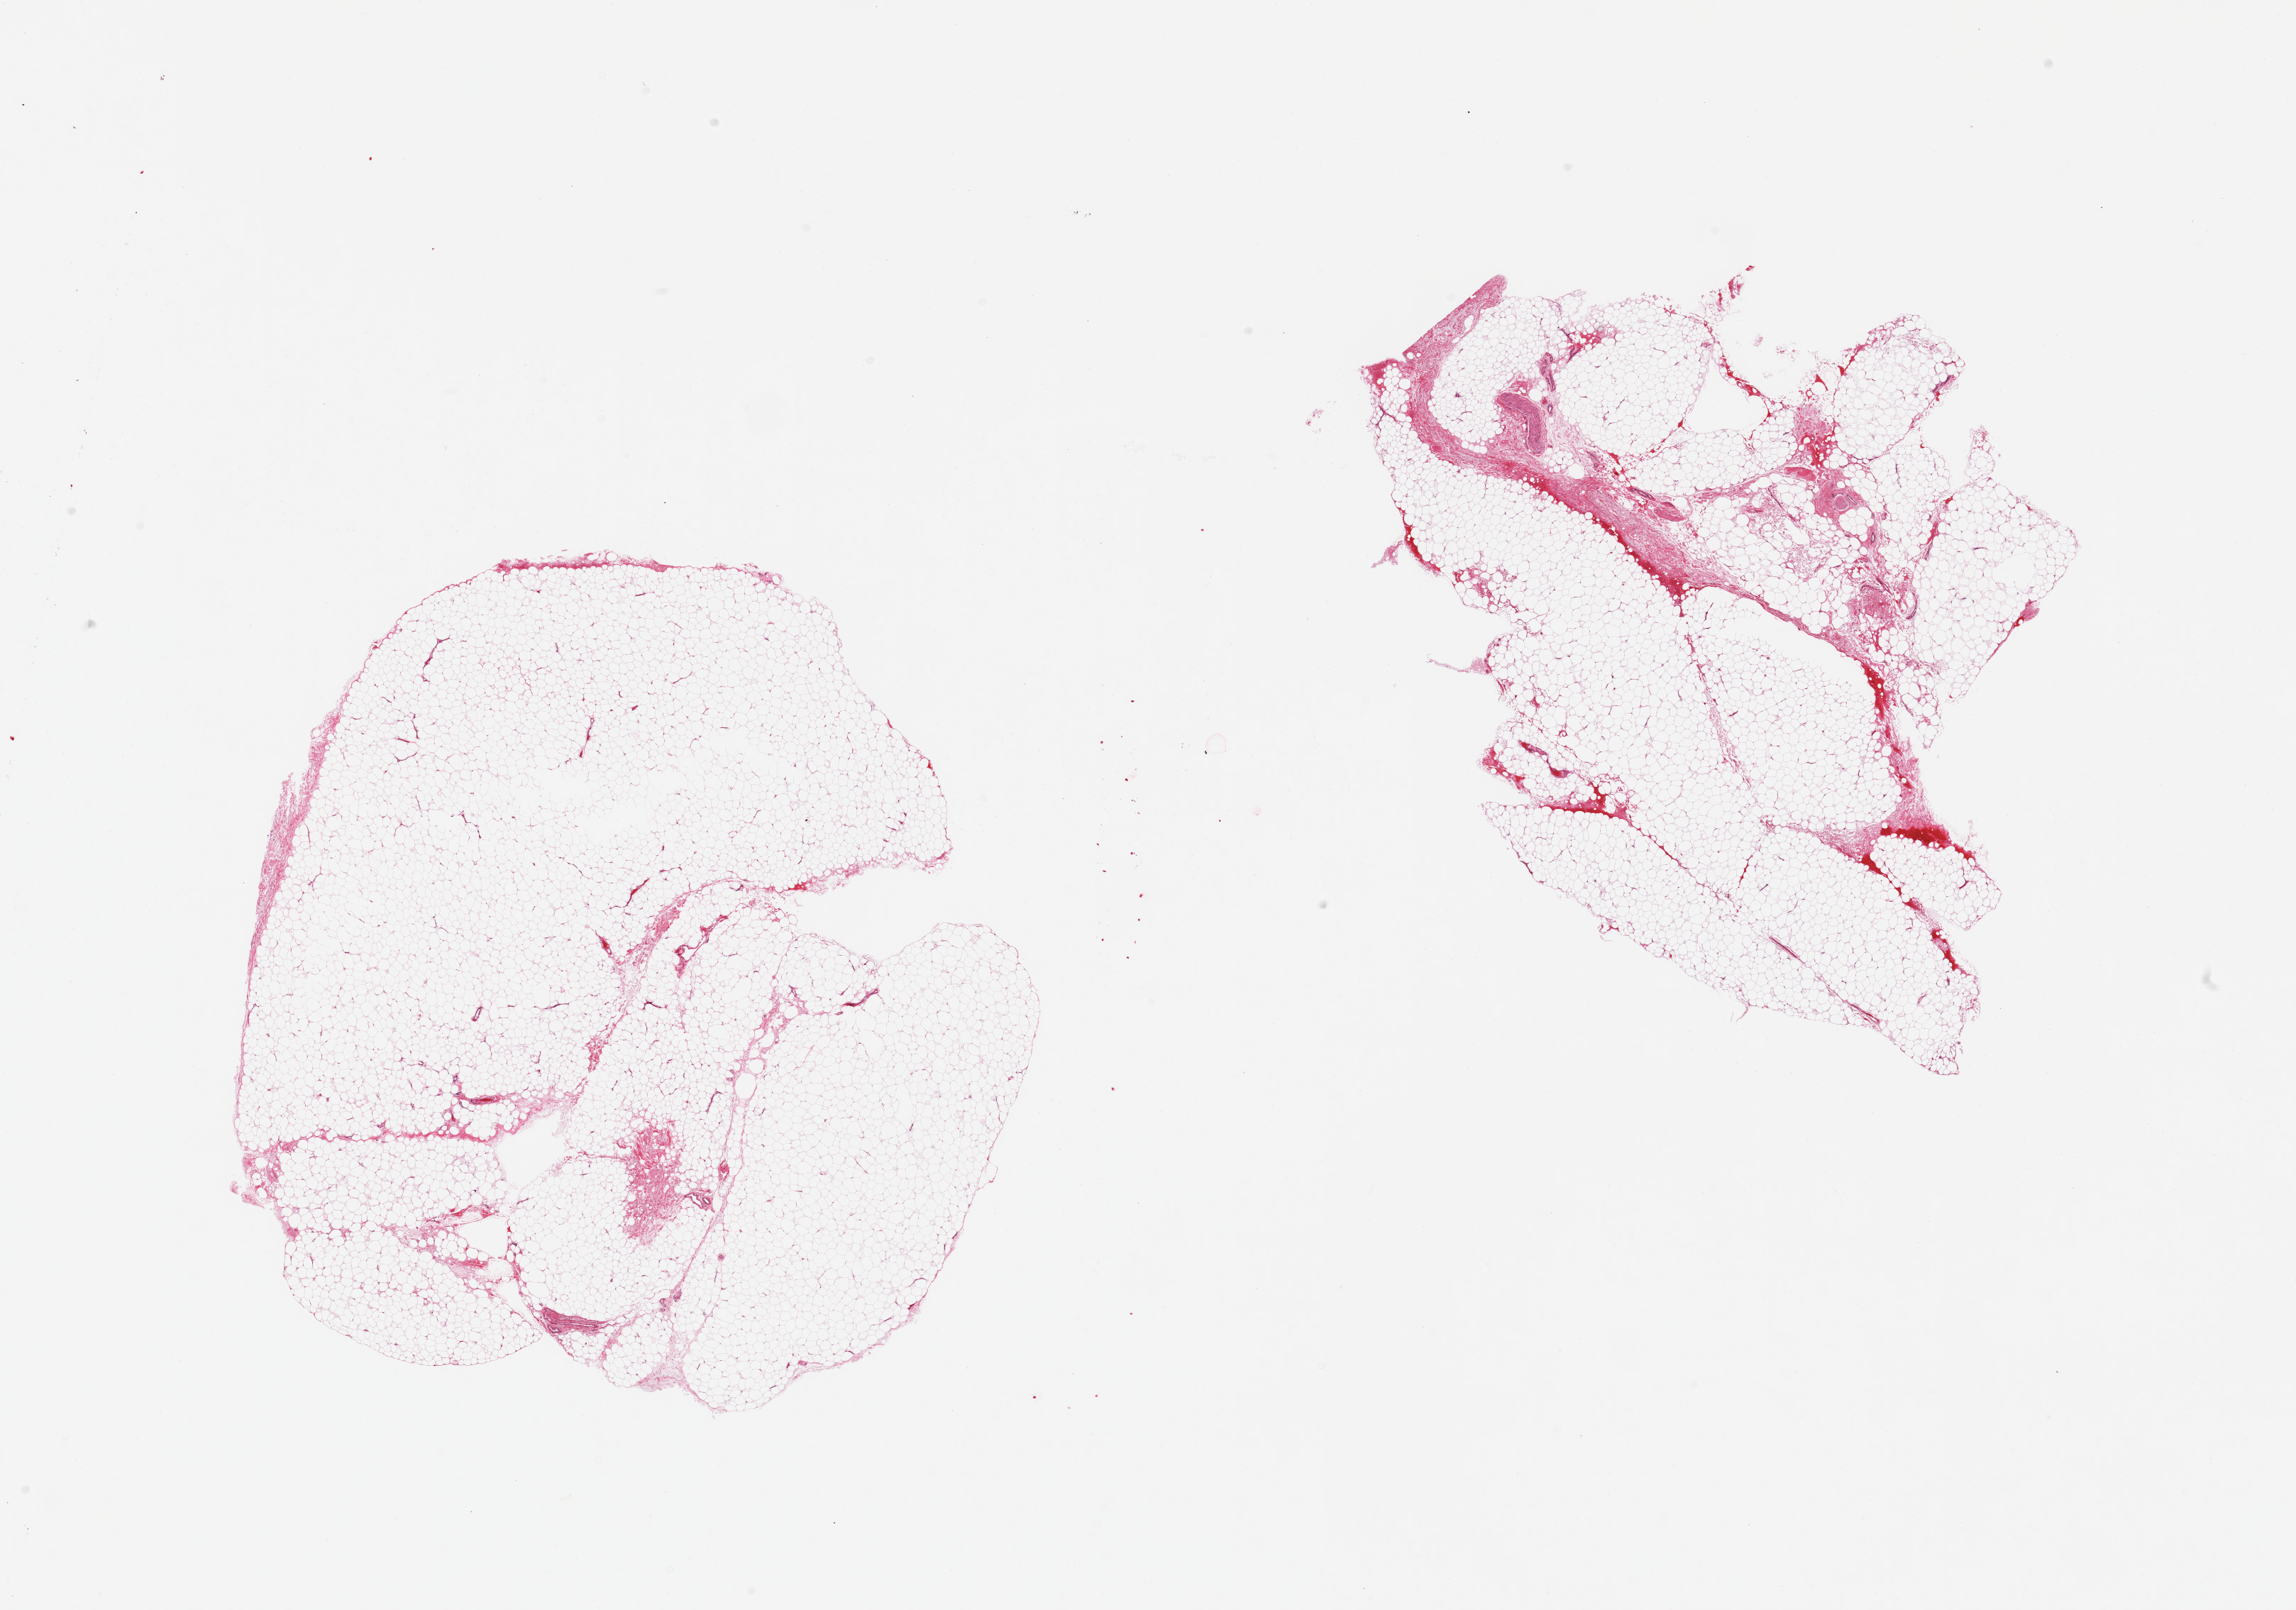
Haematoxylin and eosin whole-slide image, whole scanned area (about 25.6 x 17.9 mm) shown as a low-resolution overview; PAXgene-fixed, paraffin-embedded tissue; sampled site (target tissue): adipose tissue; donor tissue sample. Donor sex: male.
Pathologist's review note for this sample: 2 pieces, 10-15% fascia/peripheral nerve elements.